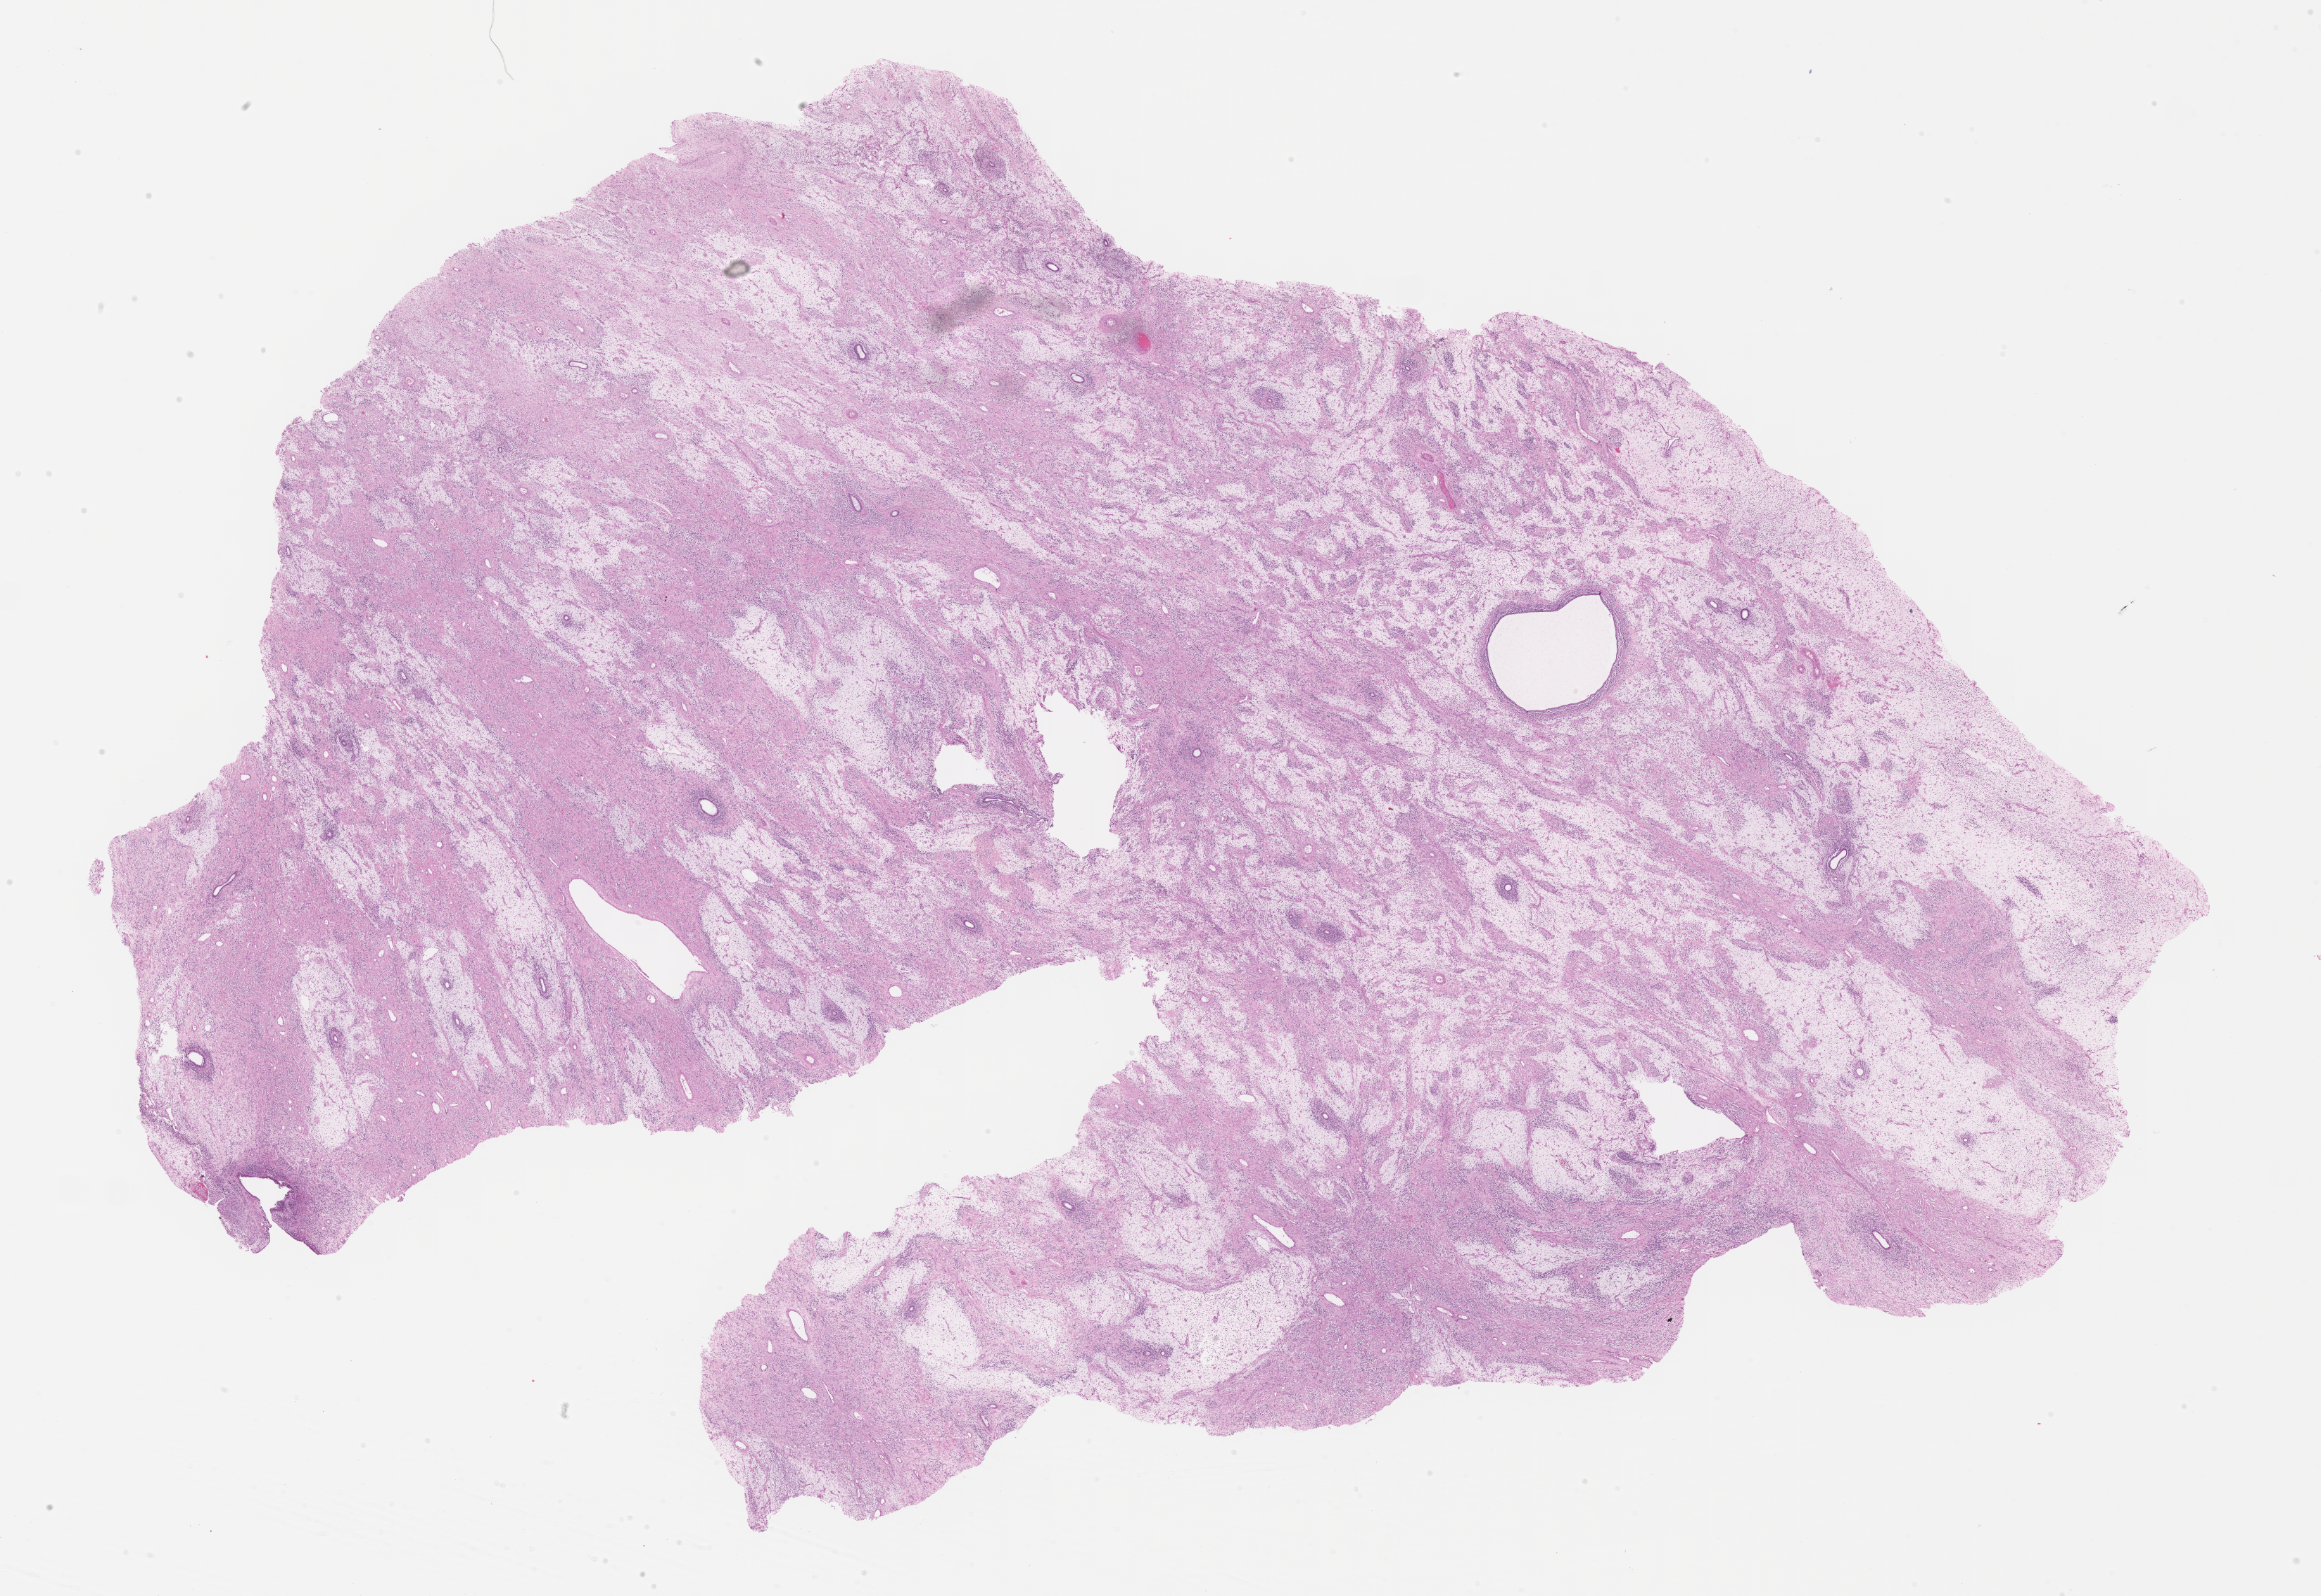
Digitized hematoxylin and eosin (H&E)-stained section of tumor tissue, whole scanned area (about 26.7 x 18.3 mm) shown as a low-resolution overview. Formalin-fixed paraffin-embedded section. Sample anatomic site: uterus. Female patient, age at diagnosis 17.1 years.
Stage (as recorded): 1. Diagnosis: rhabdomyosarcoma; histological classification: embryonal rhabdomyosarcoma. Metastatic status at presentation (as recorded): non-metastatic (confirmed).